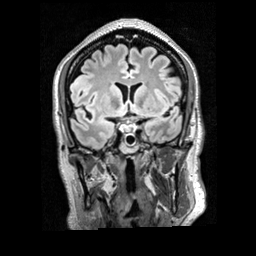
Brain MRI from a brain-tumour surgery series, one coronal slice; position 120 of 200 along the scan axis; T2 FLAIR; 256 × 256 image matrix, field of view 256 × 256 mm. Case-level facts recorded for this patient, not image findings: histopathology: Glioblastoma; WHO grade: 4; IDH mutation: no.
Annotated regions visible in this slice (expert manual segmentation):
- tumour: box from (x=70, y=73) to (x=93, y=88) px